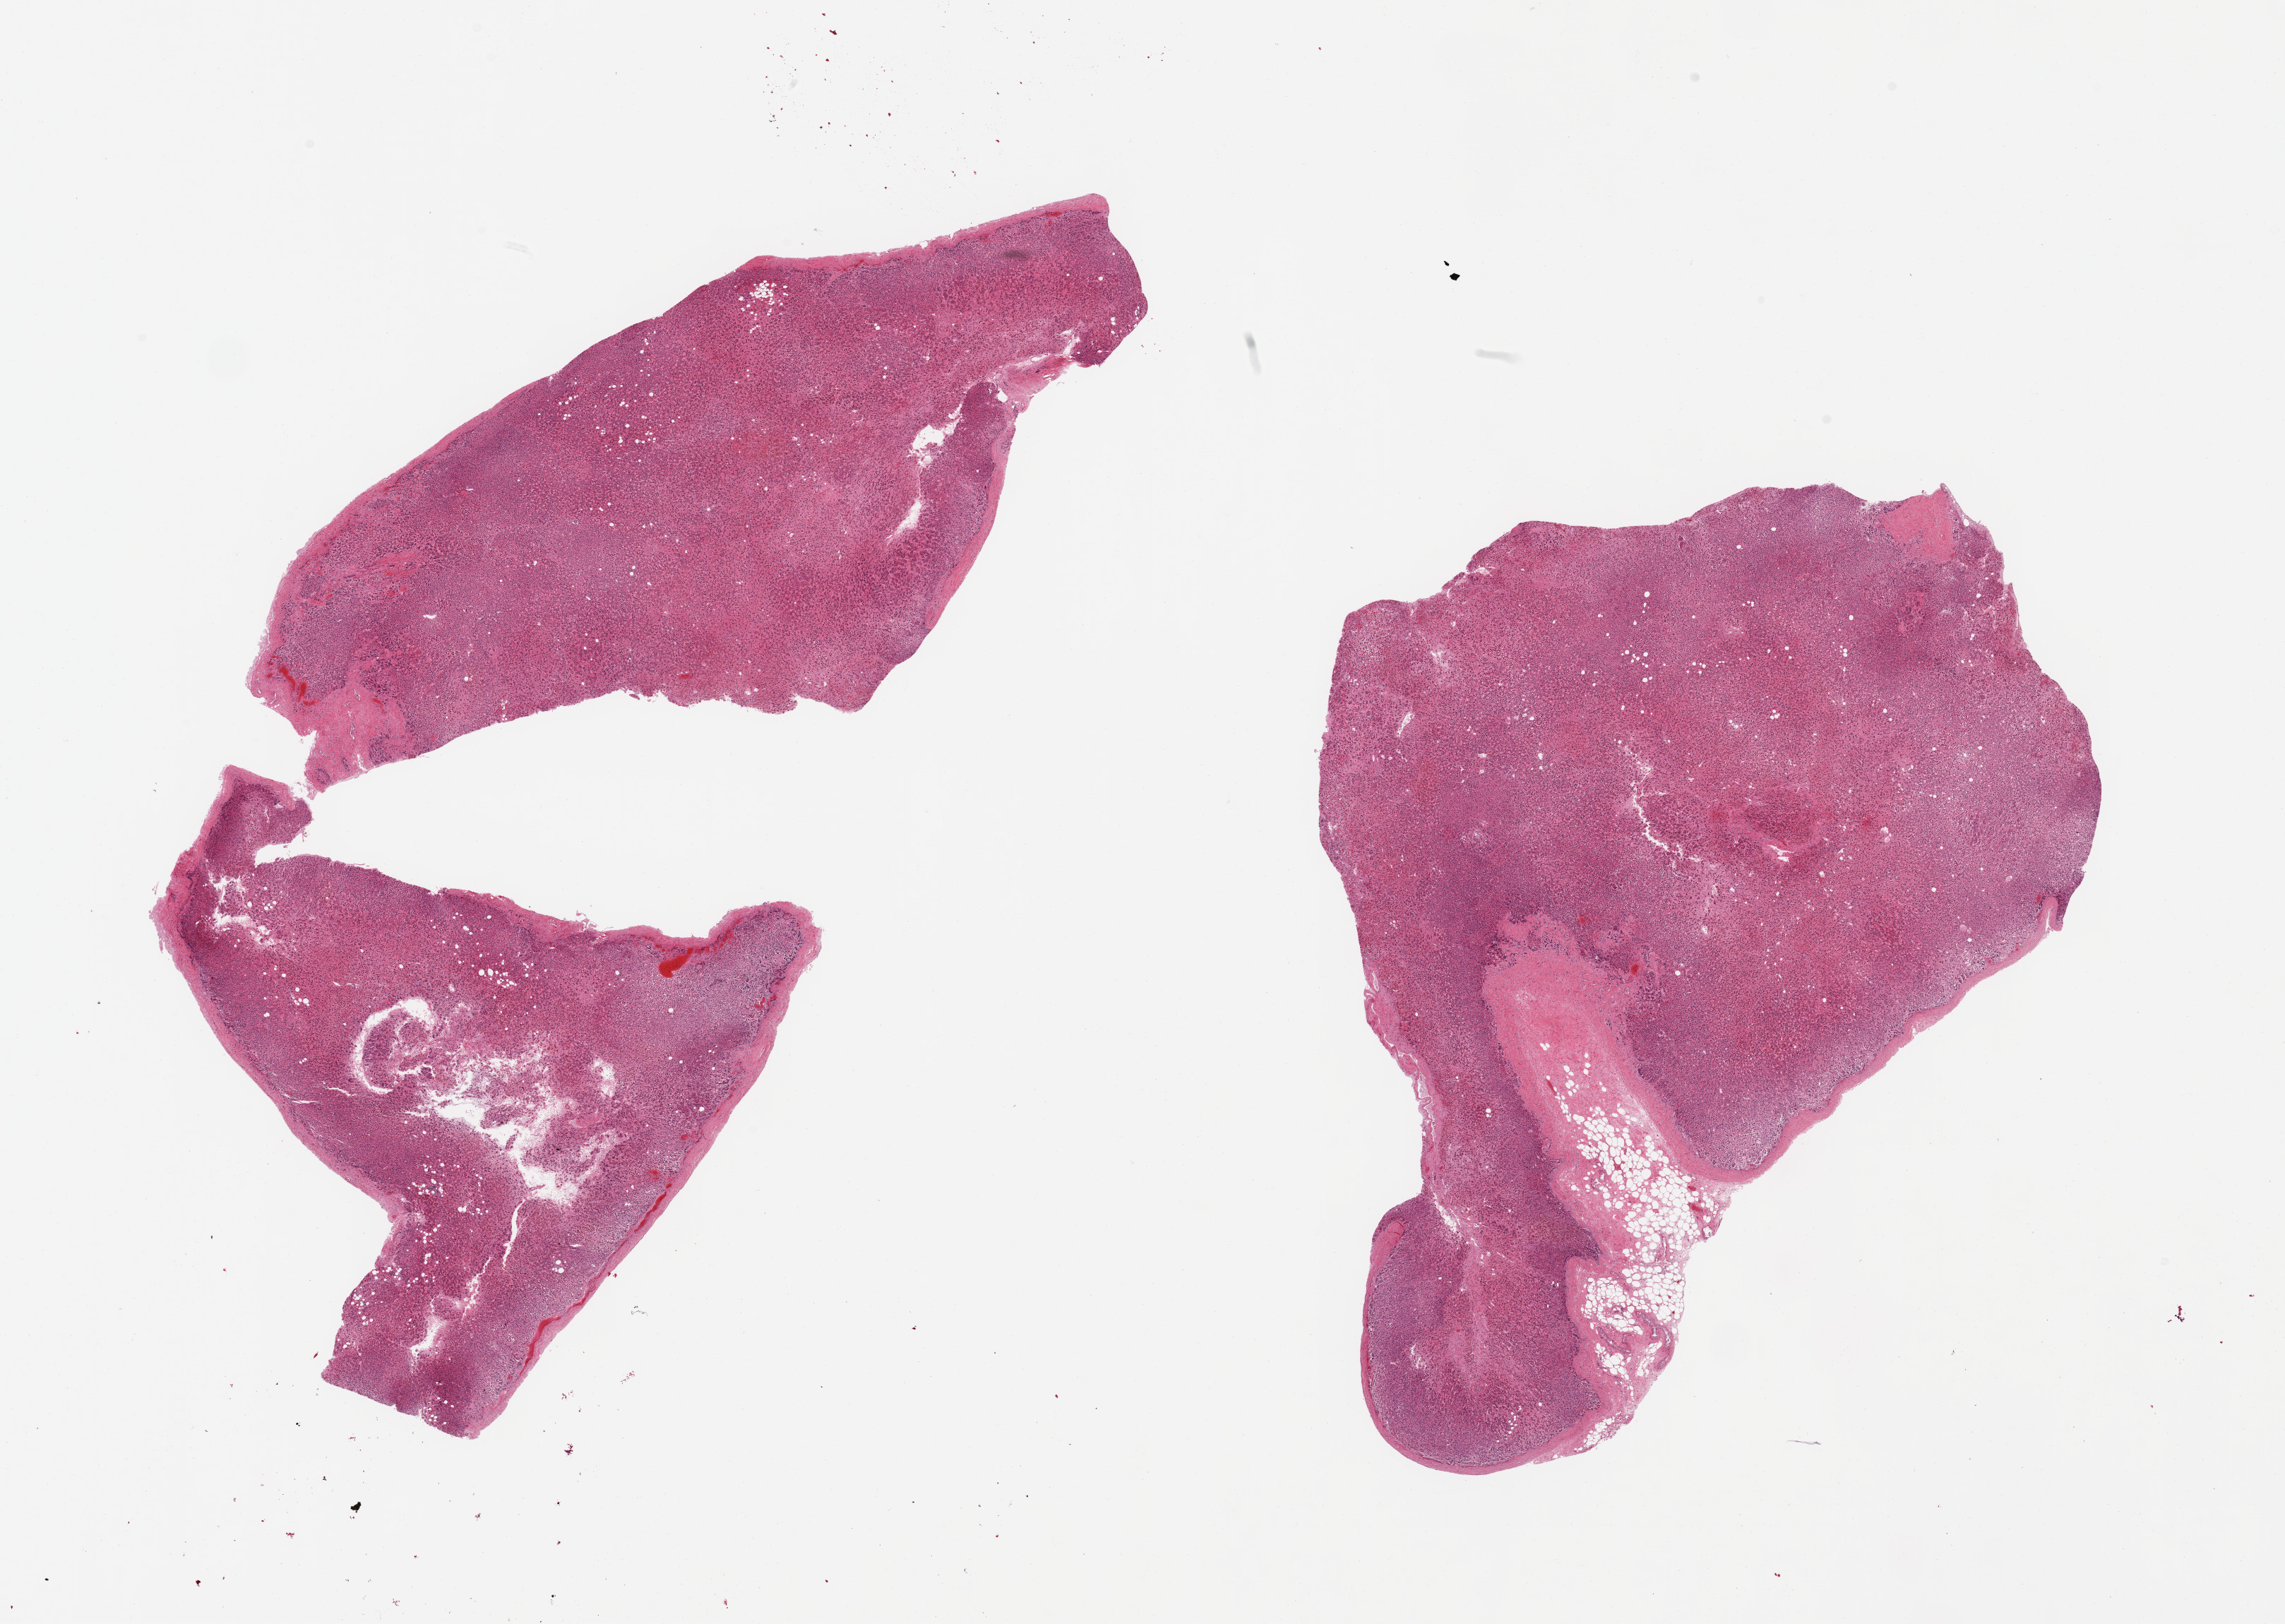
Digitized haematoxylin and eosin-stained section, low-resolution overview of the scanned area, about 25.6 x 18.2 mm; PAXgene-fixed paraffin-embedded (PFPE) section; sampled site (target tissue): adrenal gland; tissue donor sample. Male donor.
- pathologist's review note for this sample: 2 pieces; 10% fat